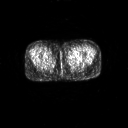
FDG PET of an extremity soft-tissue mass (from a PET/CT study), one axial slice; slice 6 of 267 in the series (ordered by position); 3.27 mm slice thickness; 128 × 128 image matrix. Patient: female, 47 years. From the clinical record (not read from this slice): histological type: myxofibrosarcoma; grade: intermediate; site of the primary tumour: left thigh.
Outlined on this slice (expert contour drawn on MRI and transferred to this co-registered scan by the dataset authors):
- gross tumour volume including surrounding oedema: bounding box [x1, y1, x2, y2] px = [69, 53, 81, 60]